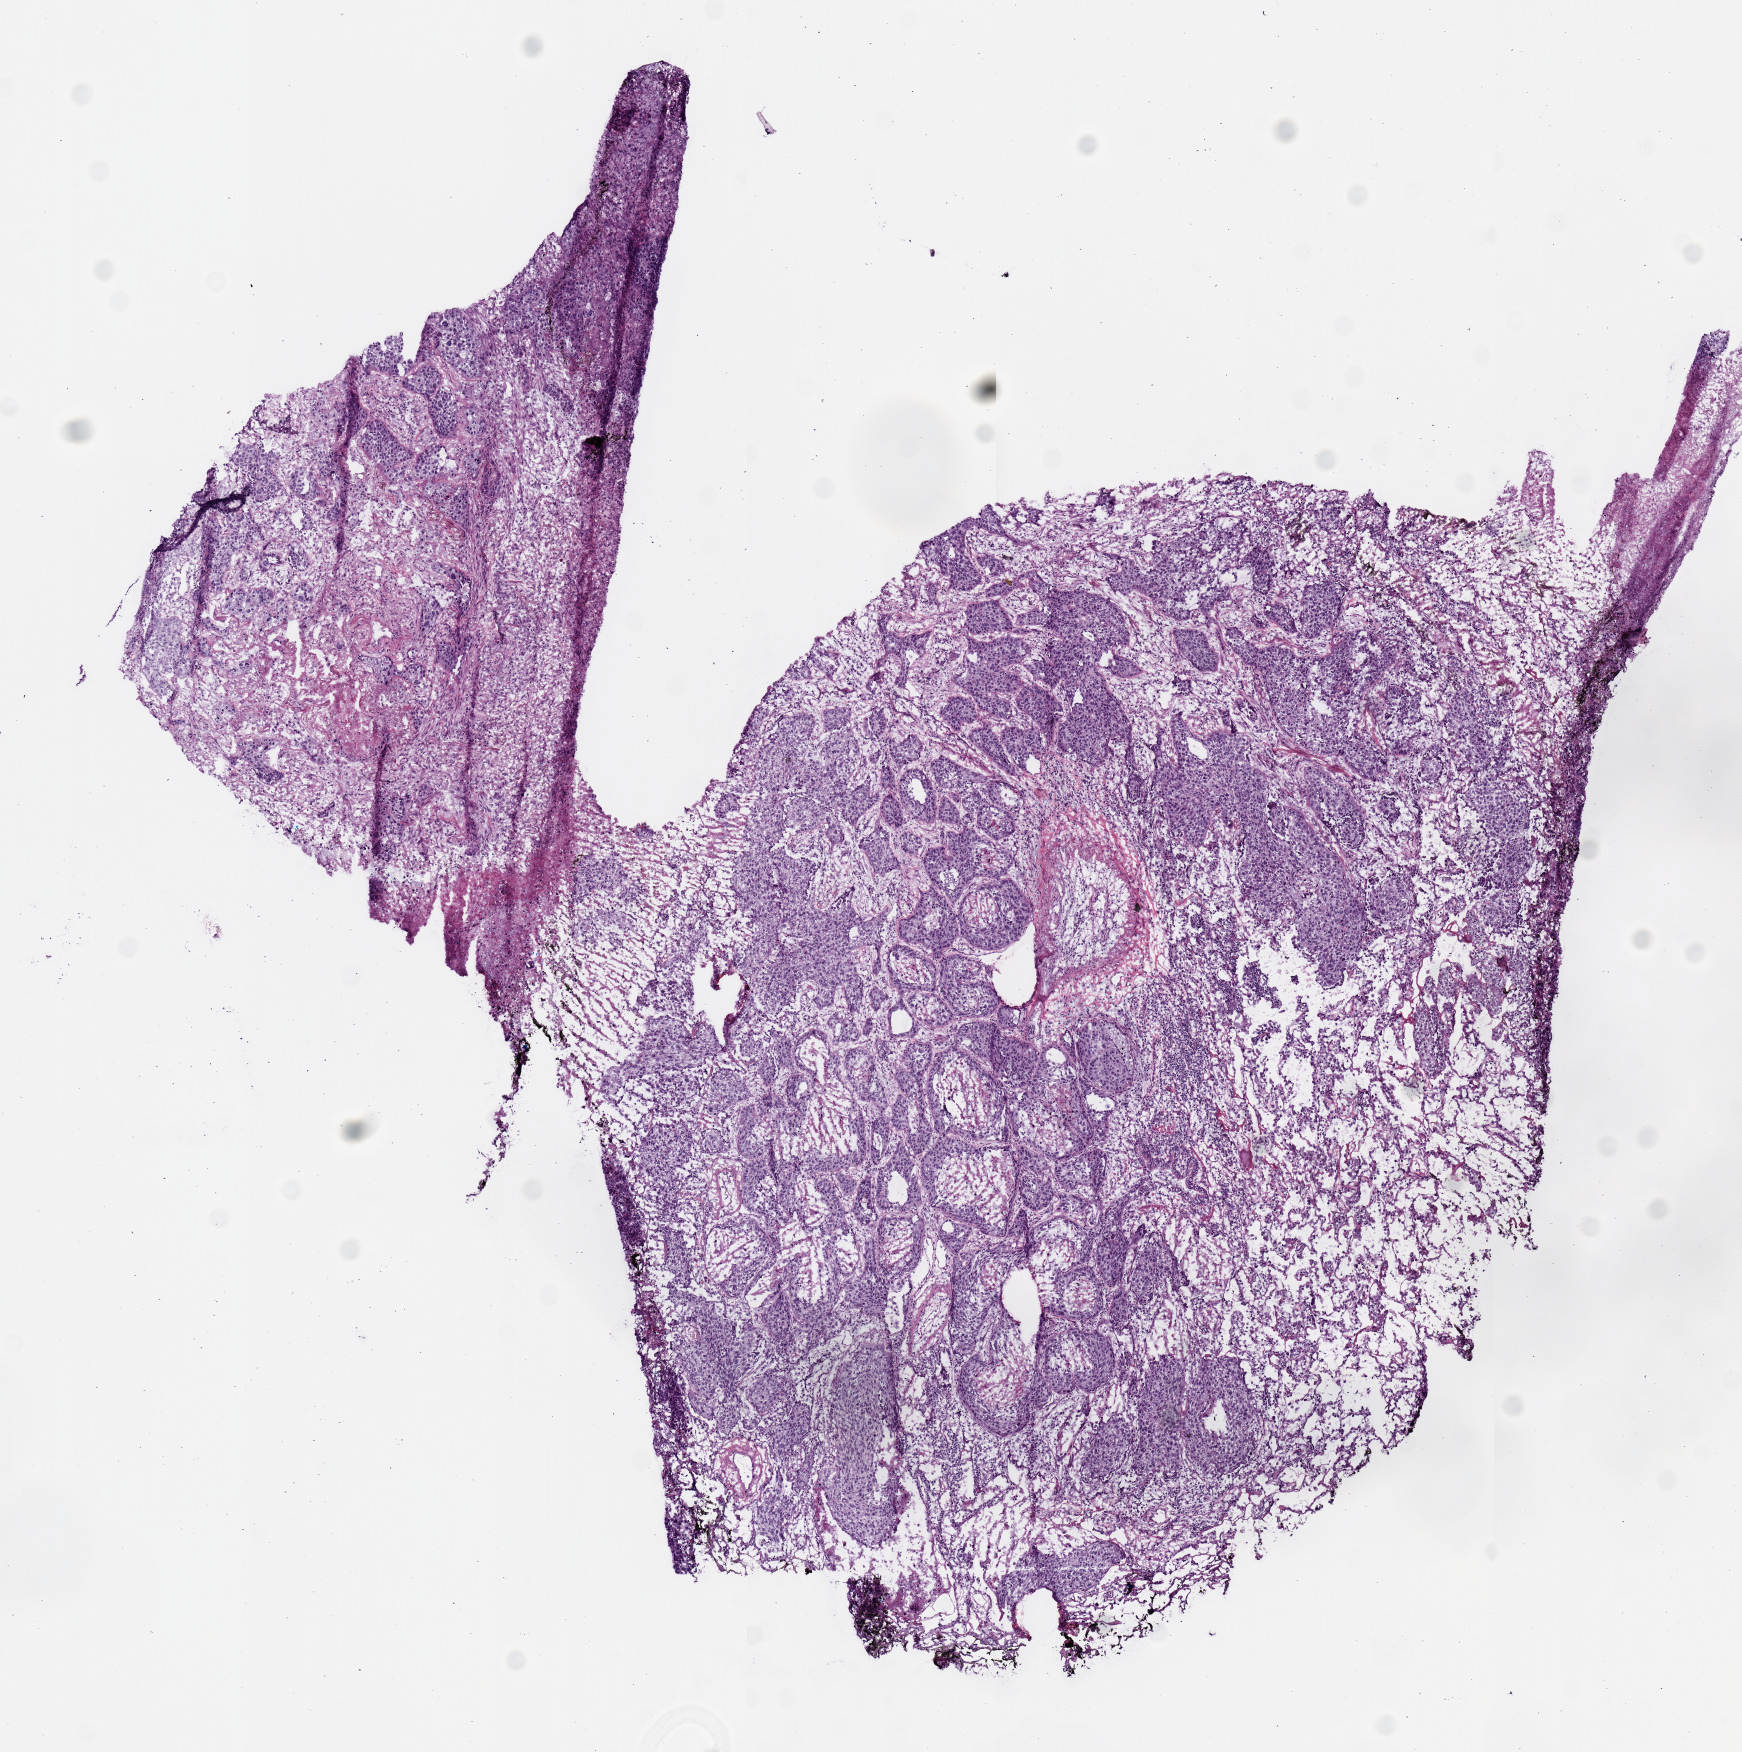
Whole-slide histology image, Hematoxylin and eosin (H&E) stained, low-resolution overview of the scanned area, about 6.9 x 6.9 mm (acquisition: 20x scan); frozen section from the top of the tissue portion; lung, primary tumour sample. Male patient; age at initial diagnosis 76 years. Composition of this section per pathologist review: tumour cells 80%, tumour nuclei 75%, normal cells 20%, stromal cells 15%, necrosis 5%.
Pathologic diagnosis: Adenocarcinoma, NOS (upper lobe, lung). Laterality: left. AJCC pathologic stage: IB (7th edition).